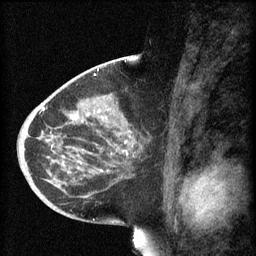
Breast MRI (dynamic contrast-enhanced), one sagittal slice; slice 34 of 60 in the series (ordered by position); 3 images stored at this slice position (order not interpretable as contrast timing); 1.5 T; TE 4.2 ms, TR 8.1 ms; 2 mm slice thickness; 256 × 256 image matrix, field of view 200 × 200 mm. Patient: female, 44 years.
Annotated regions visible in this slice (semi-automatic segmentation, software-assisted and operator-edited):
- analysis volume of interest (the breast-tissue region the enhancement analysis was run in; not a lesion): bounding box [x1, y1, x2, y2] px = [59, 110, 151, 169]
- tumour enhancement mask (voxels above the 70 % enhancement threshold inside the analysis volume of interest): [70, 116, 128, 155]